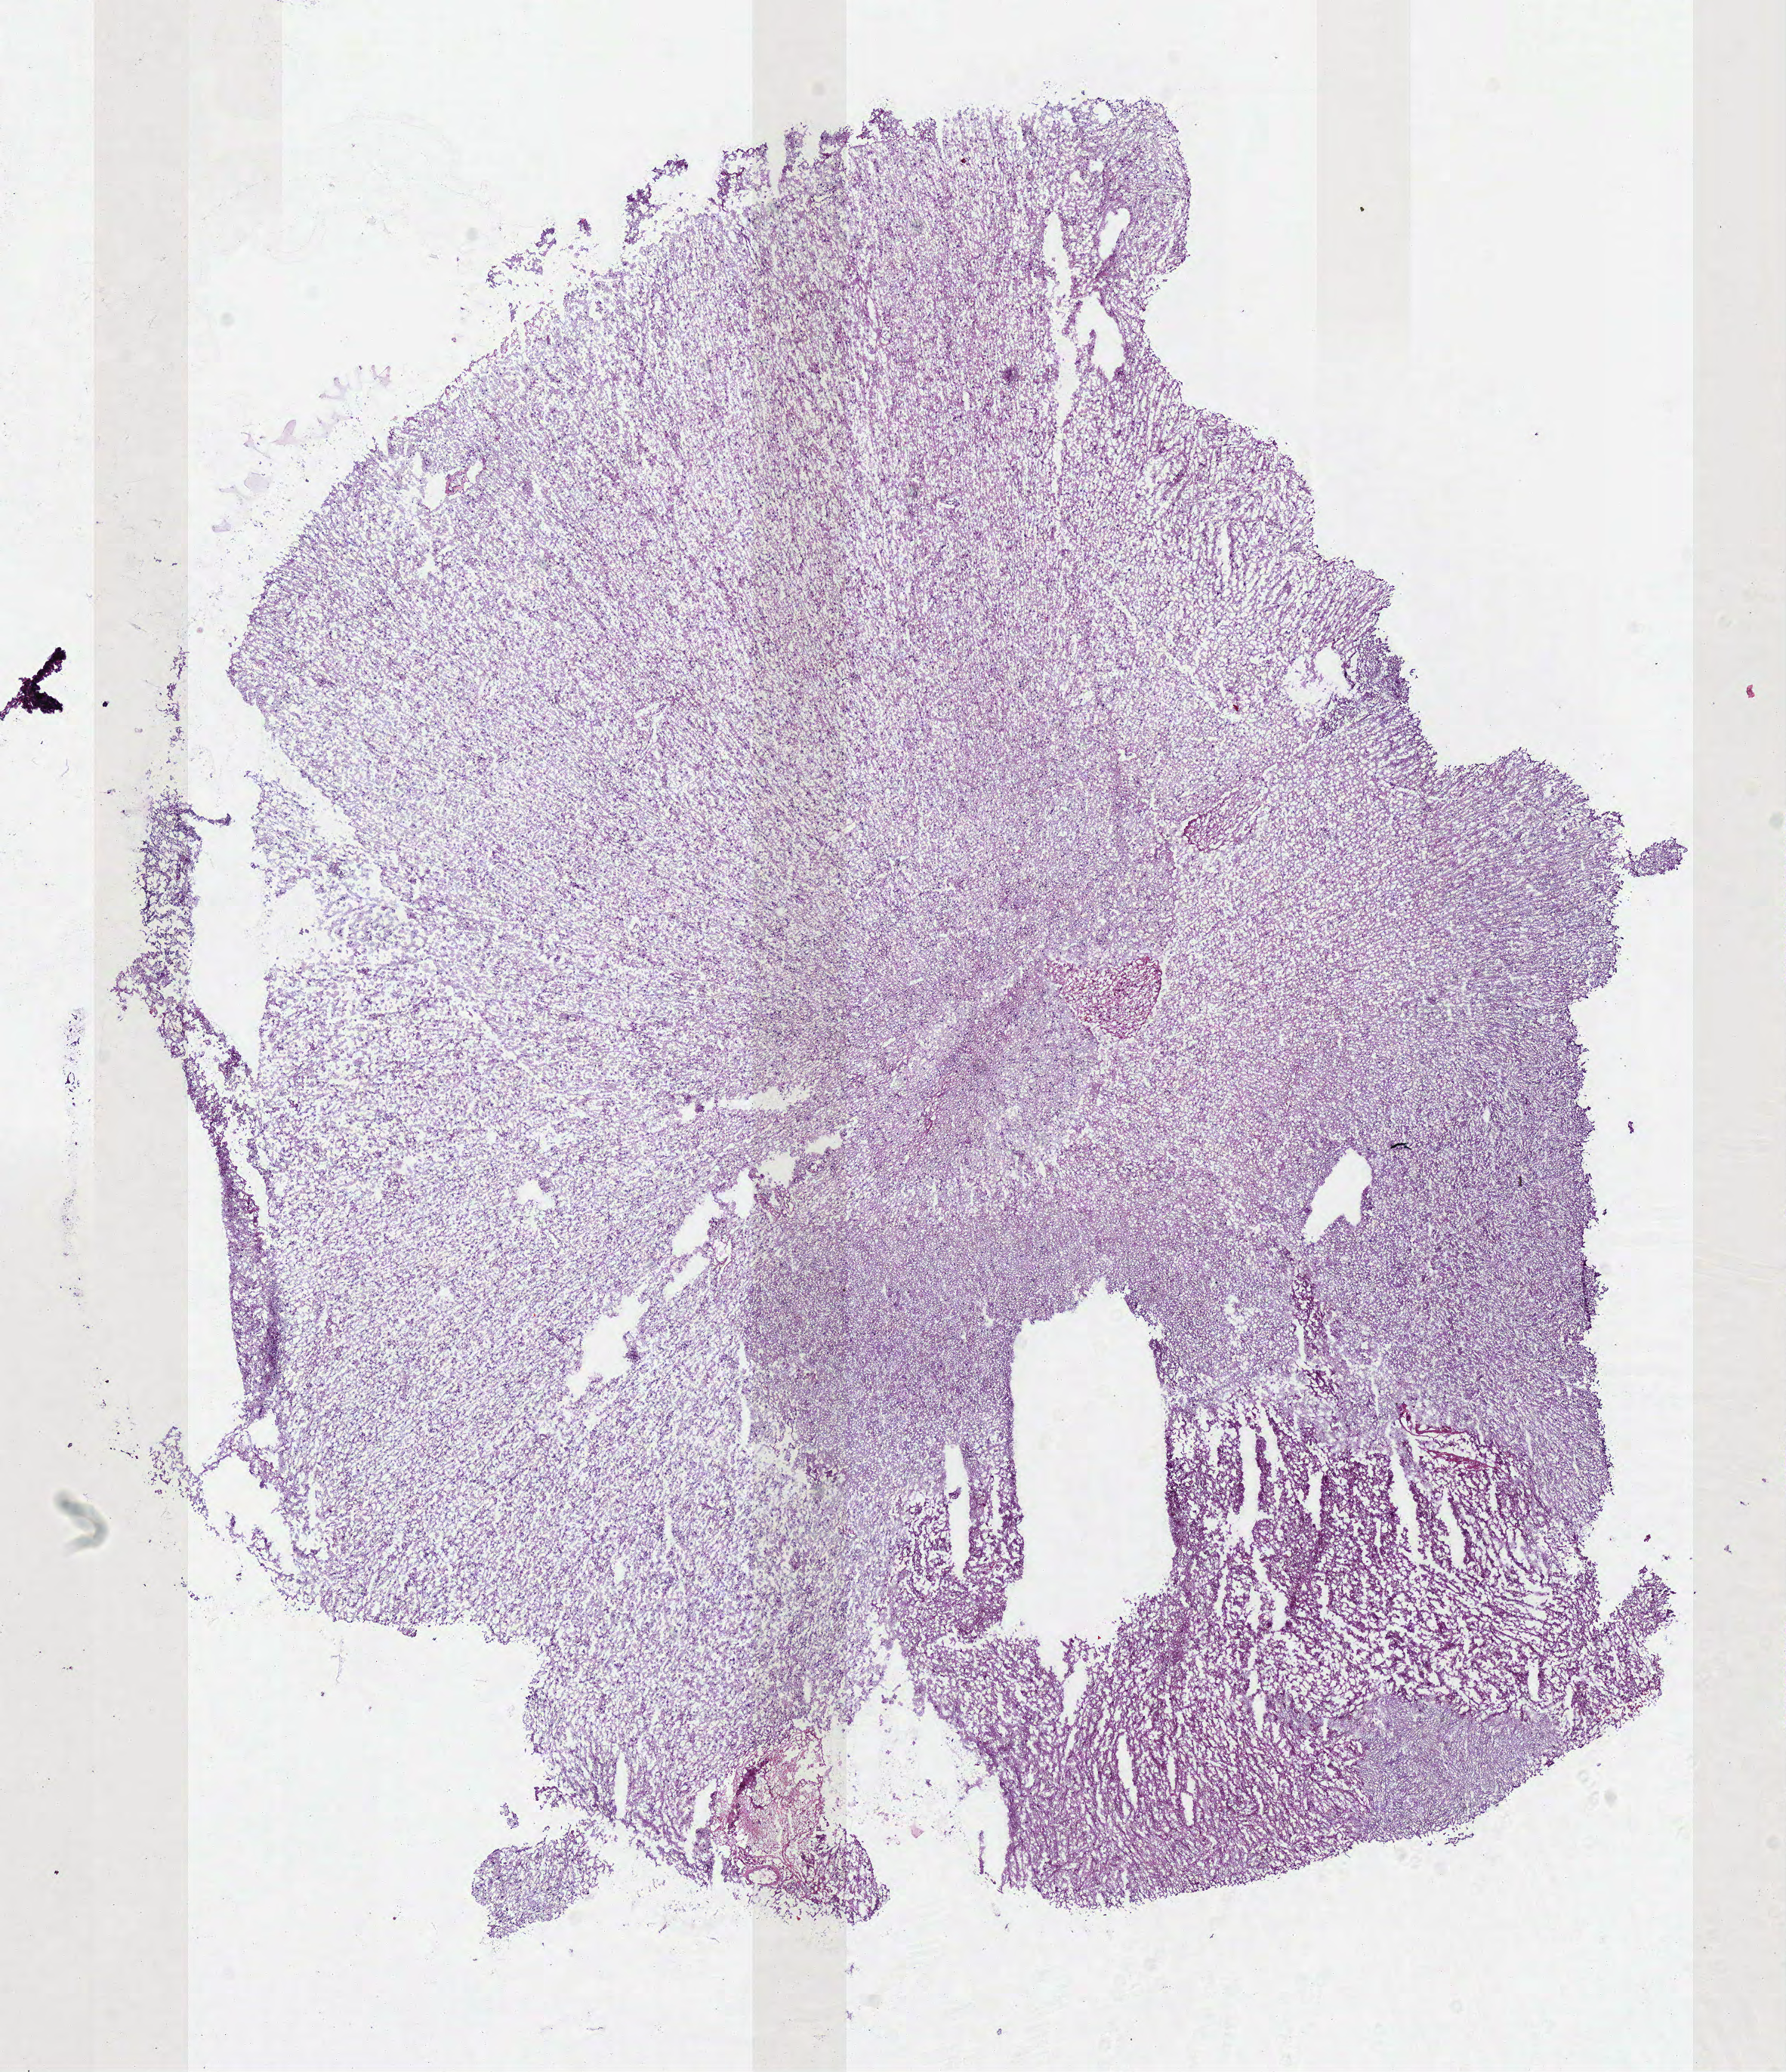
Digitized H&E-stained tissue section (whole slide), low-resolution overview of the scanned area, about 9.3 x 10.8 mm, frozen section from the top of the tissue portion, primary tumour sample from the brain. Patient: male, age at initial diagnosis 25 years. Slide review estimates, as recorded: tumour cells 100%, tumour nuclei 65%.
Diagnosis: Mixed glioma (cerebrum).